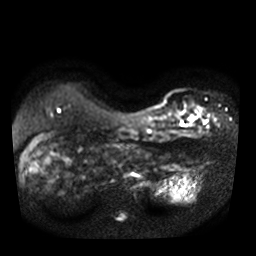
Breast MRI, one axial slice; slice 15 of 36 in the series (ordered by position); diffusion-weighted series; image 2 of 4 stored at this slice position (different b-values; order by instance number); 3 T; 256 × 256 image matrix, field of view 320 × 320 mm. Female patient.
Outlined on this slice (manually delineated by an expert):
- tumour on diffusion-weighted imaging: bounding box [x1, y1, x2, y2] px = [189, 115, 197, 121]